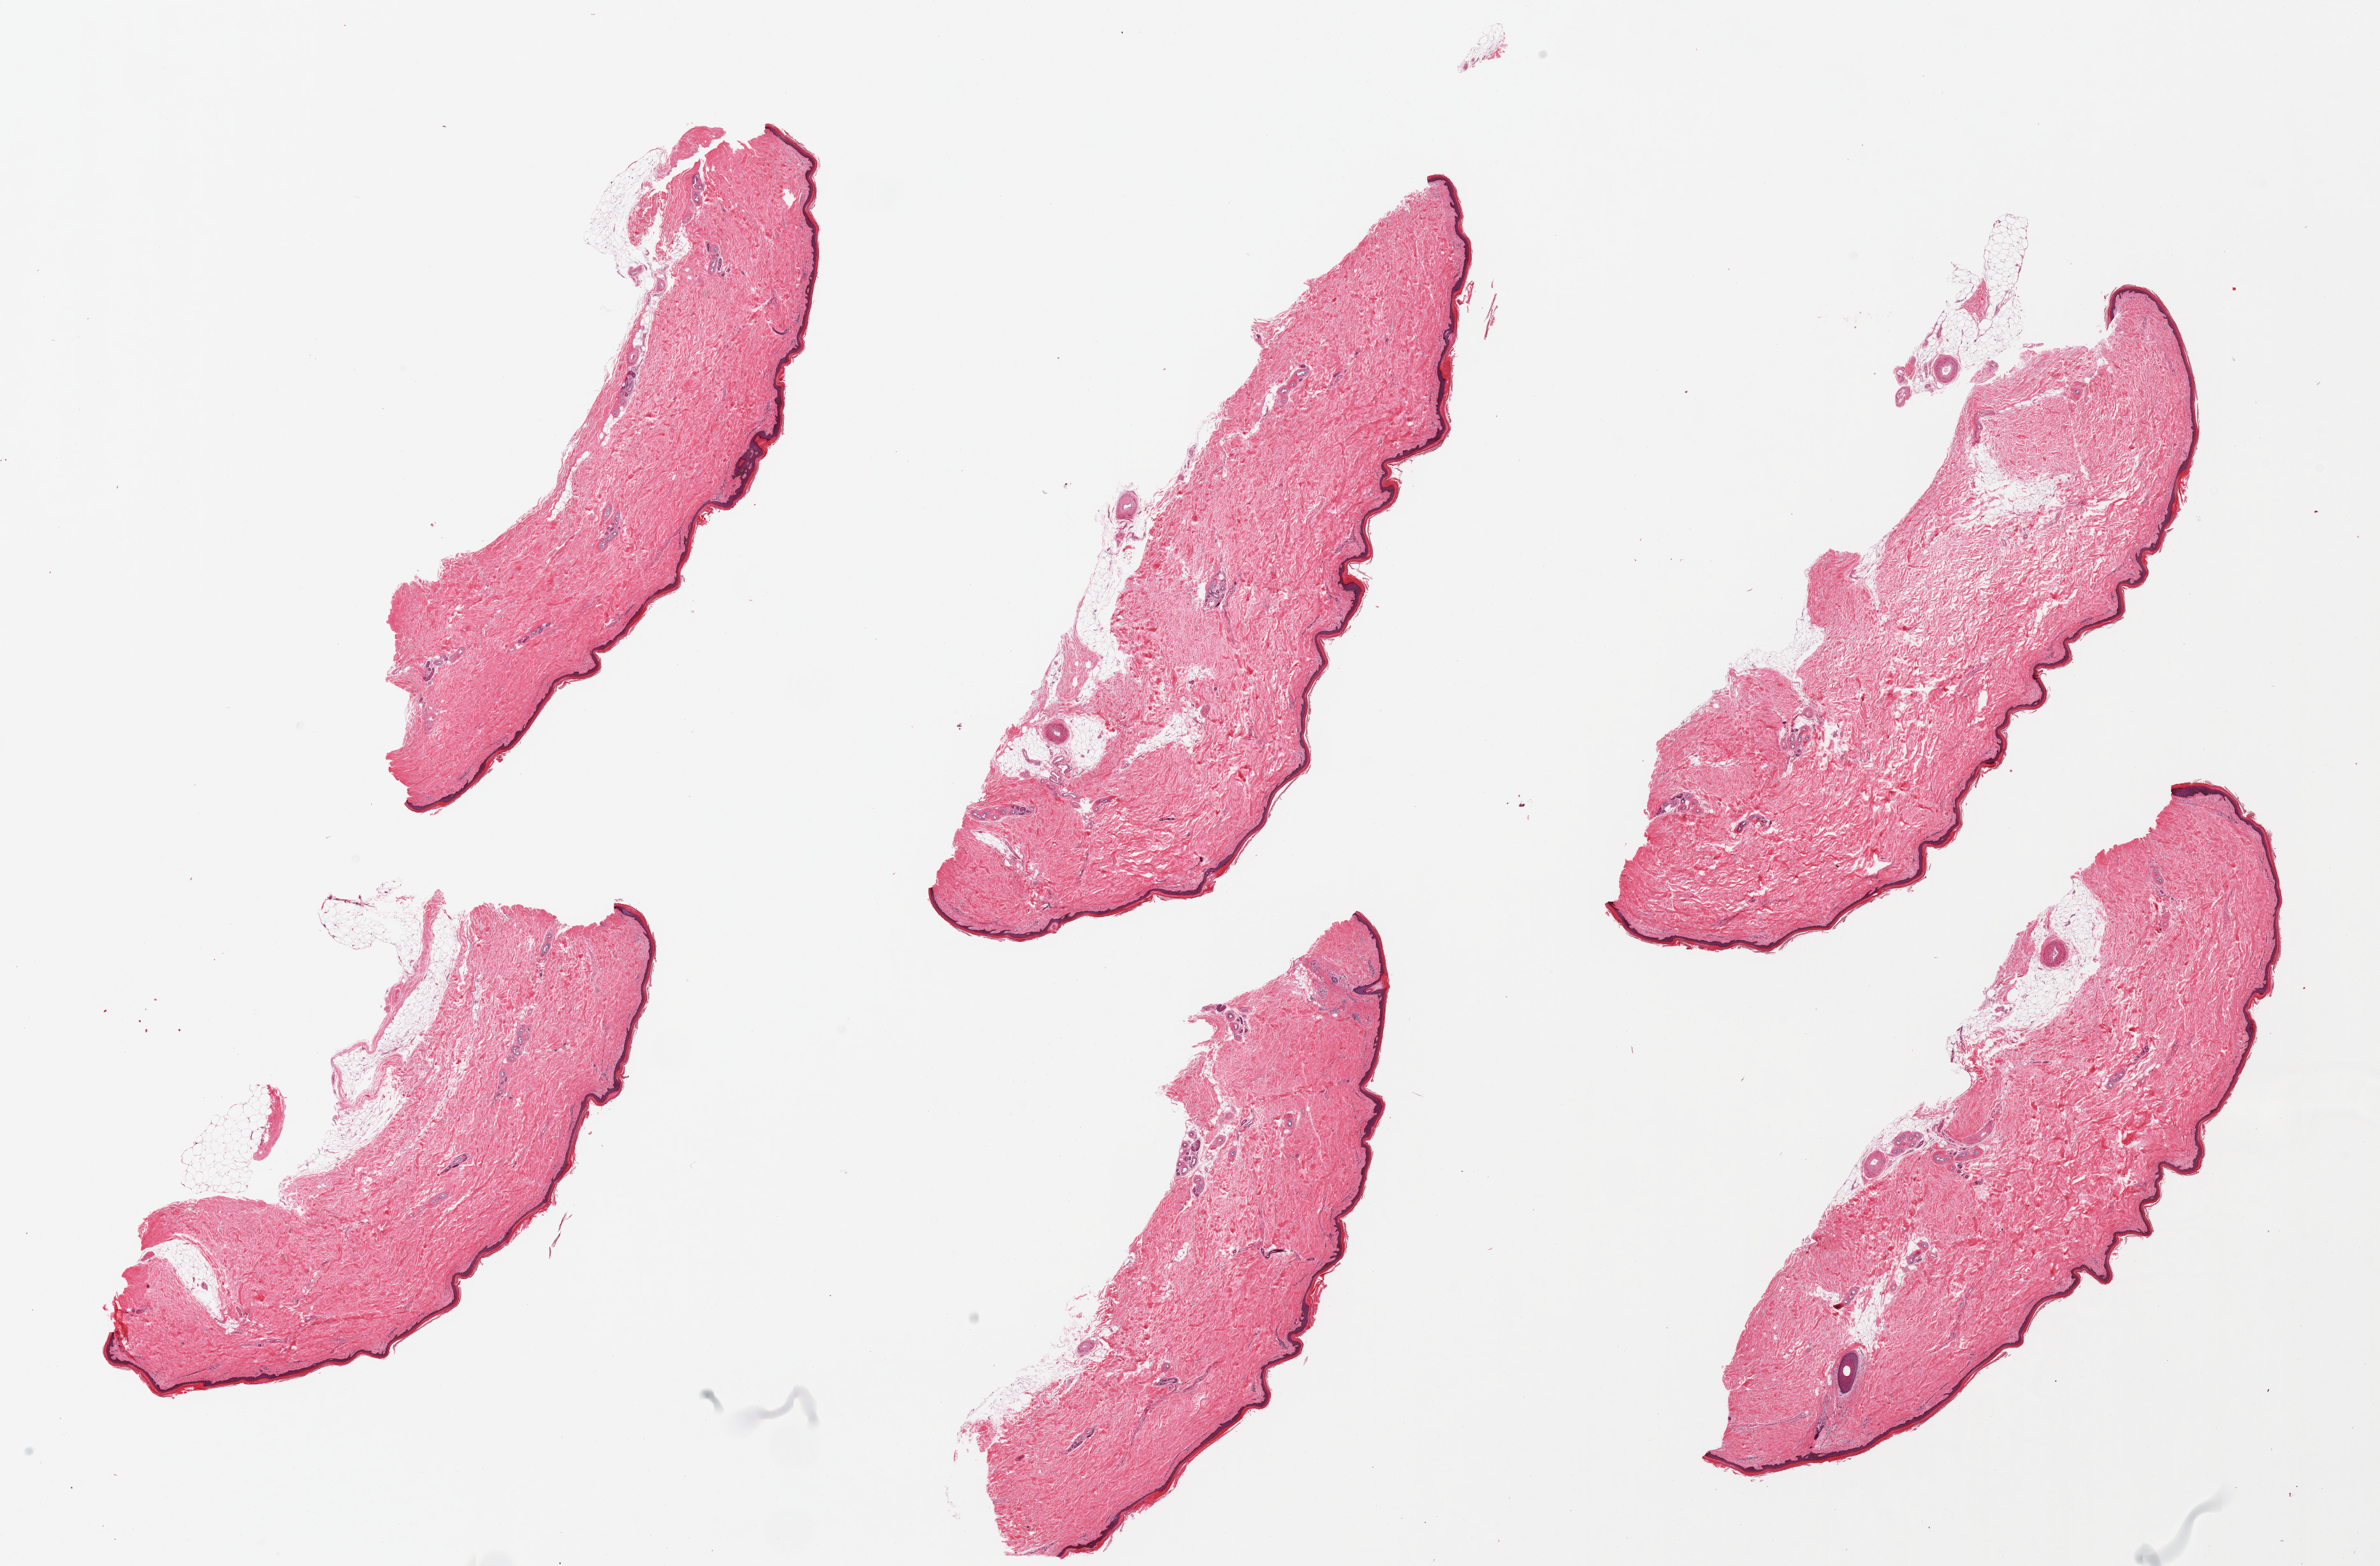
Hematoxylin and eosin (H&E) whole-slide image, shown as a low-resolution overview of the whole scanned area (about 29.5 x 19.4 mm, slide scanned at 20x). PAXgene-fixed paraffin-embedded (PFPE) section. Sampled site (target tissue): skin of lower leg. Donor tissue sample.
- reviewer comment on this tissue sample: 6 pieces; small amount of subcutaneous fat